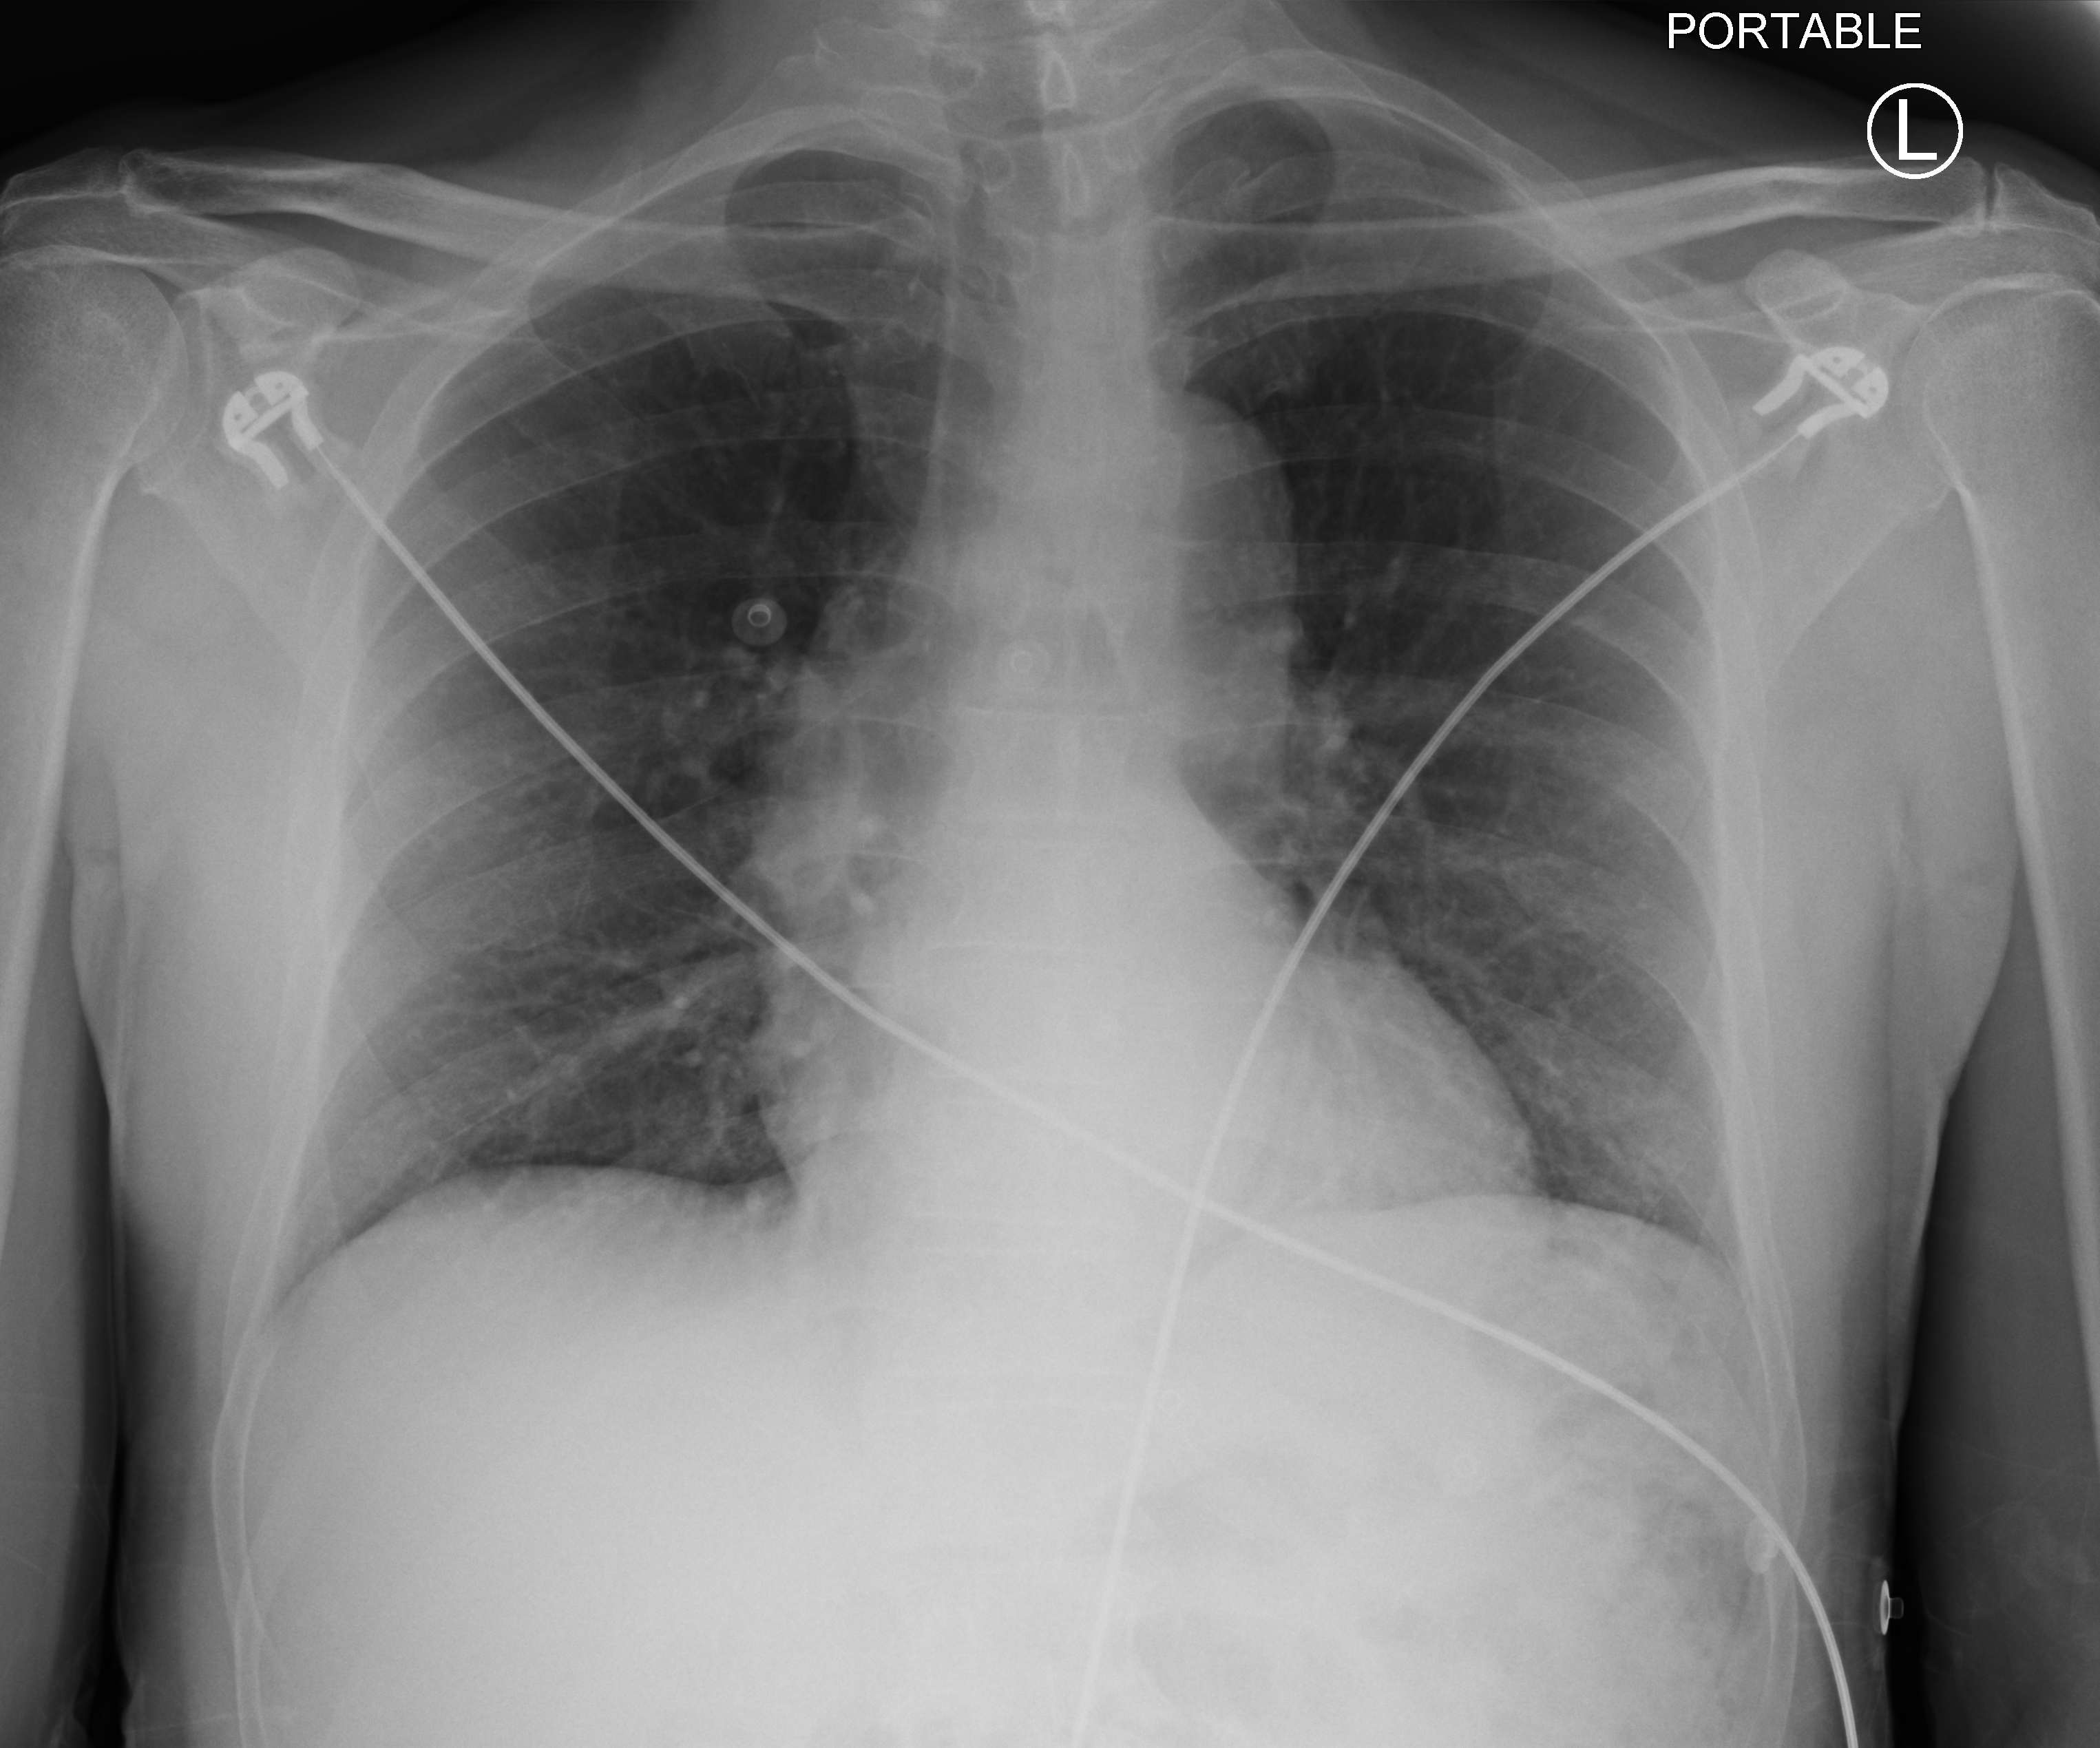
Chest X-ray (portable), anteroposterior (AP) projection. Patient hospitalised with COVID-19; male, aged 60–74 years.
Hospital-stay facts (about this admission, not read from this image; timing relative to this image not recorded): admitted to intensive care during this hospital stay: no; hypertension (admission record): no.